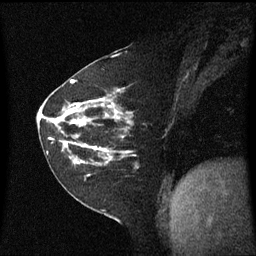
Breast MRI (dynamic contrast-enhanced), one sagittal slice. Position 27 of 60 along the scan axis. Dynamic contrast-enhanced series, image 2 of 3 at this slice position (ordered by acquisition). 1.5 T. TE 4.2 ms, TR 8.4 ms. 2 mm slice thickness. 256 × 256 image matrix, field of view 210 × 210 mm. Female patient, age 60 years. Case-level facts recorded for this patient, not image findings: setting: breast cancer imaged before/during neoadjuvant chemotherapy; receptor status: triple-negative.
Structures marked on this image (semi-automatically segmented with operator editing):
- analysis volume of interest (the breast-tissue region the enhancement analysis was run in; not a lesion): bounding box <45,99,137,182> (left, top, right, bottom; pixels)
- tumour enhancement mask (voxels above the 70 % enhancement threshold inside the analysis volume of interest): <51,100,119,161>